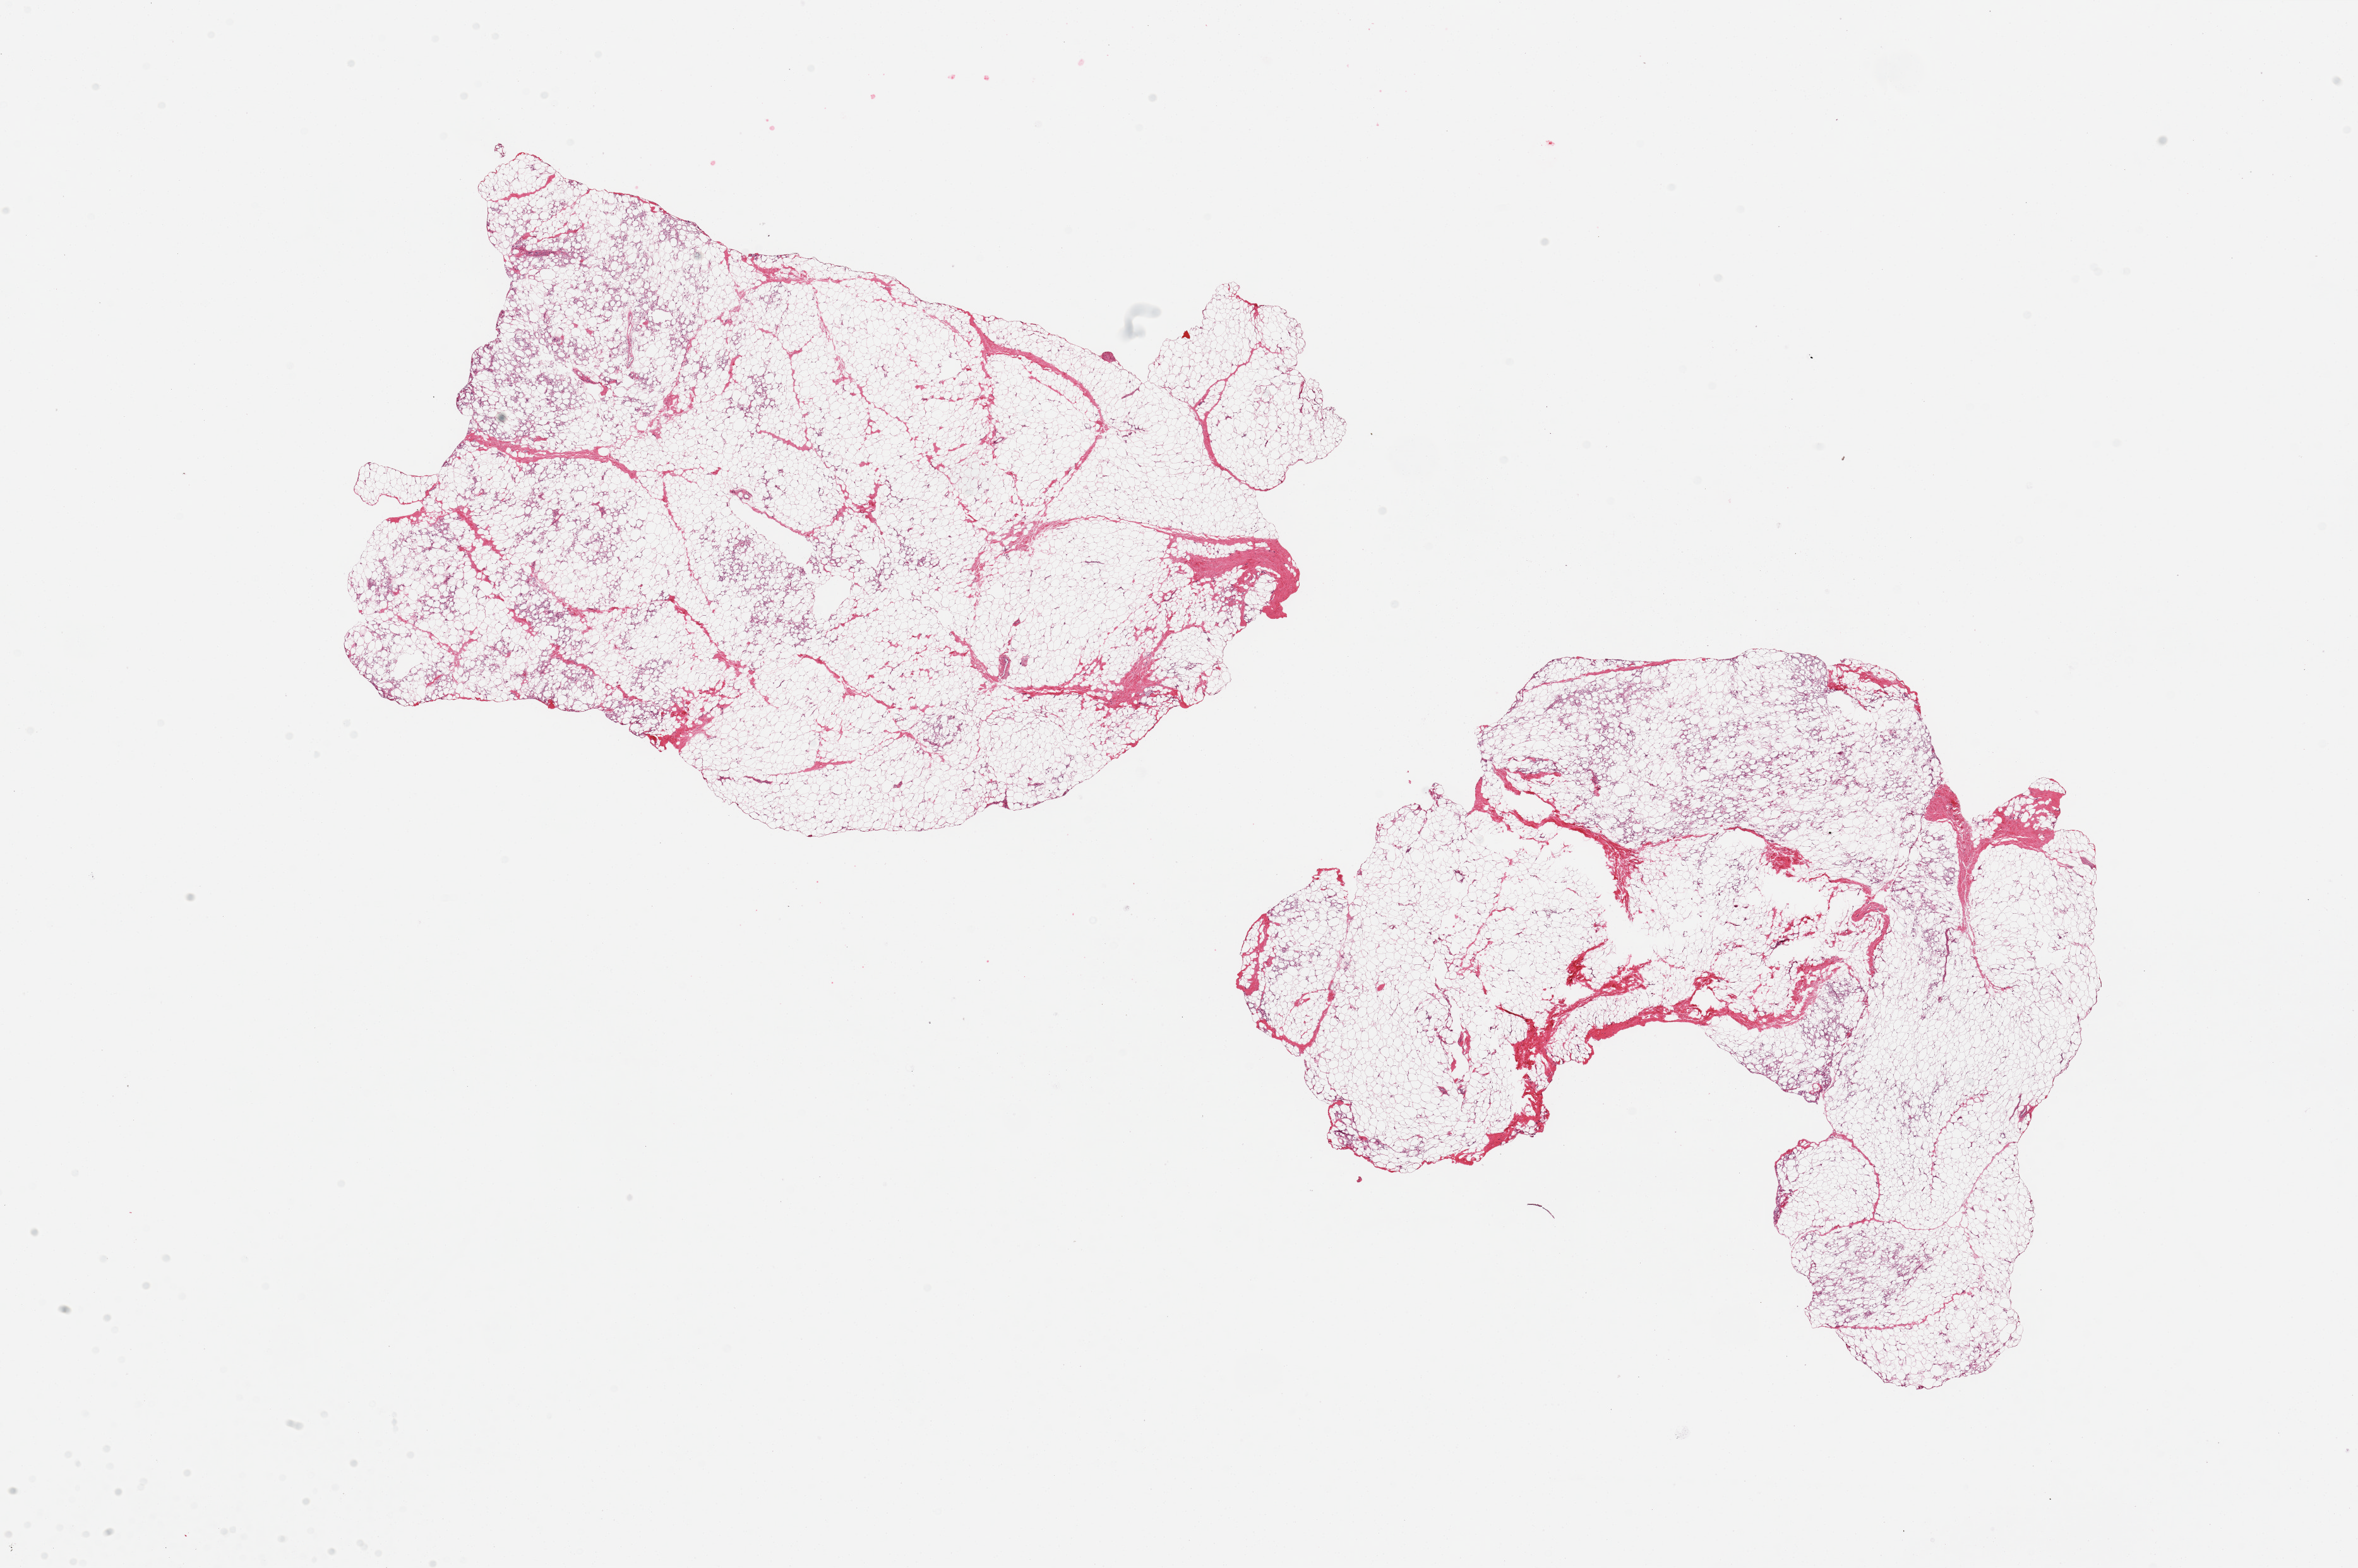
Hematoxylin and eosin (H&E) whole-slide image — shown as a low-resolution overview of the whole scanned area (about 29.5 x 19.6 mm), PAXgene-fixed paraffin-embedded (PFPE) section, sampled site (target tissue): breast, donor tissue sample. Donor sex: male.
Pathologist's review note for this sample: 2 pieces; small foci of fat necrosis; no ducts.